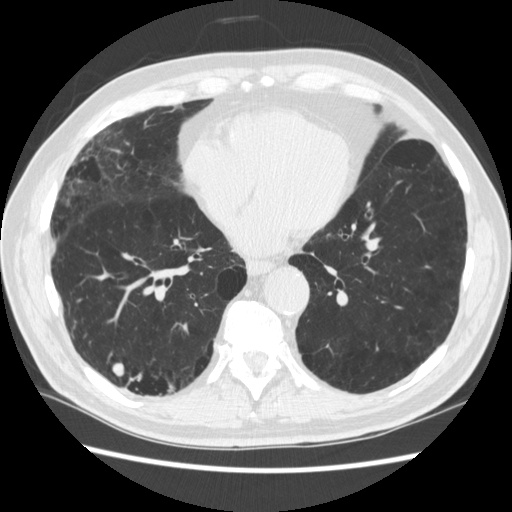
Chest CT (low-dose screening protocol), one axial image; third annual screen; lung window (W 1500 / L -600 HU). Male participant, aged 70 years at enrolment. Former smoker at enrolment.
Expert reader's lesion annotation, bounding box <130,359,176,413> (left, top, right, bottom; pixels). The screening reader recorded 4 non-calcified nodules or masses ≥4 mm on this exam (right lower lobe, right lower lobe, left lower lobe, left lower lobe); which of them this box marks is not recorded.